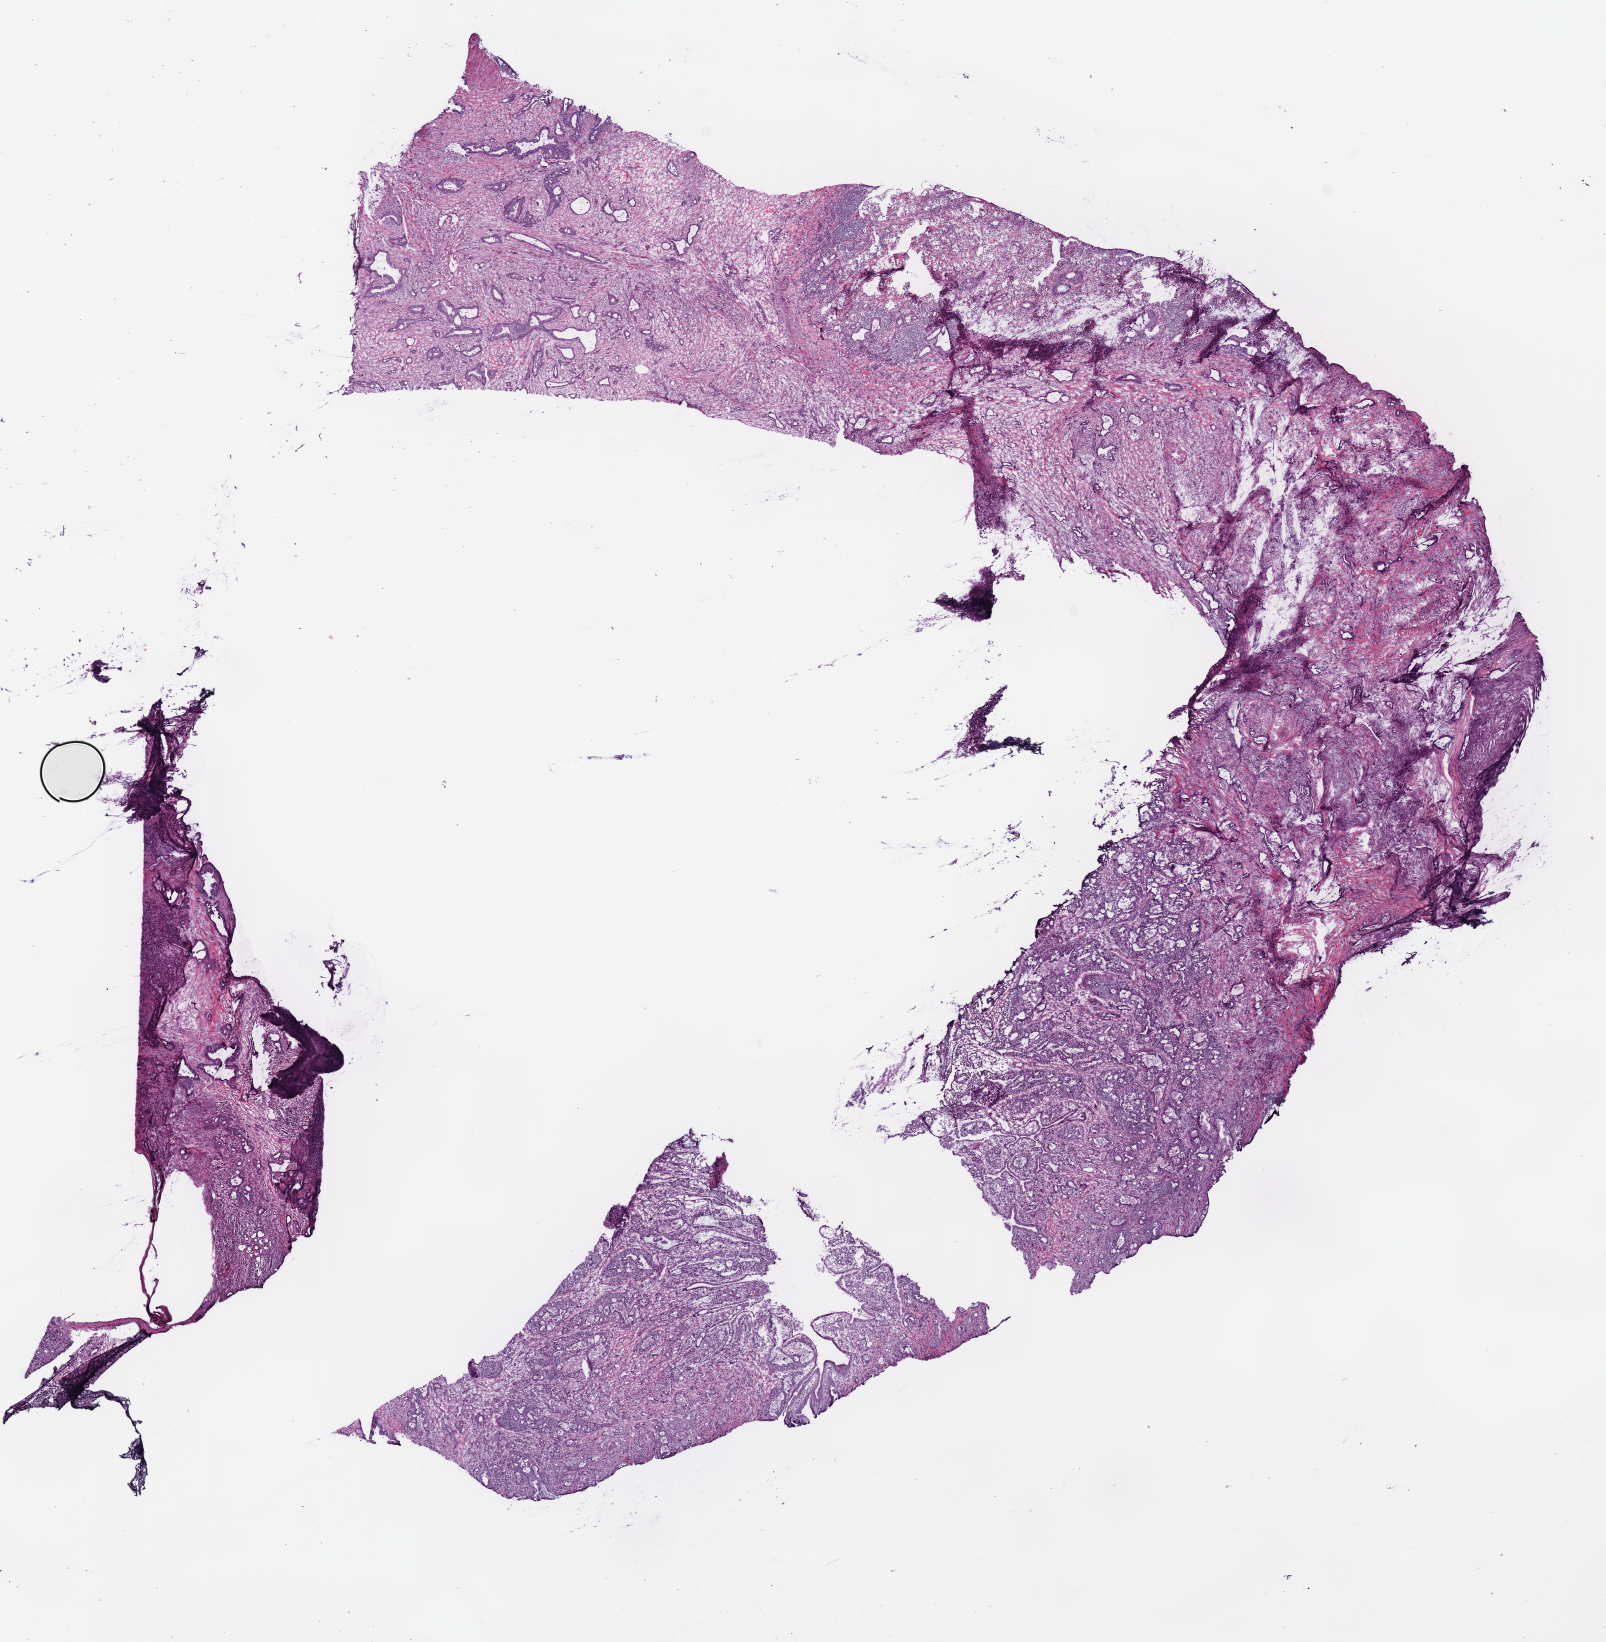
Whole-slide histology image, Hematoxylin and eosin (H&E) stained, shown as a low-resolution overview of the whole scanned area (about 12.7 x 12.9 mm, from a 40x scan). Frozen section from the bottom of the tissue portion. Sample: primary tumour, pancreas. Male, age 80 years at initial diagnosis. Histologic grade: G3 (poorly differentiated). Pathologist review of this section (percent, as recorded): tumour cells 68%, tumour nuclei 60%, normal cells 0%, stromal cells 30%, necrosis 2%.
Lymph nodes positive (case pathology): 4 of 11 examined. AJCC pathologic stage: IIB (7th edition). TNM: T3 N1 M0. Pathologic diagnosis: Infiltrating duct carcinoma, NOS.